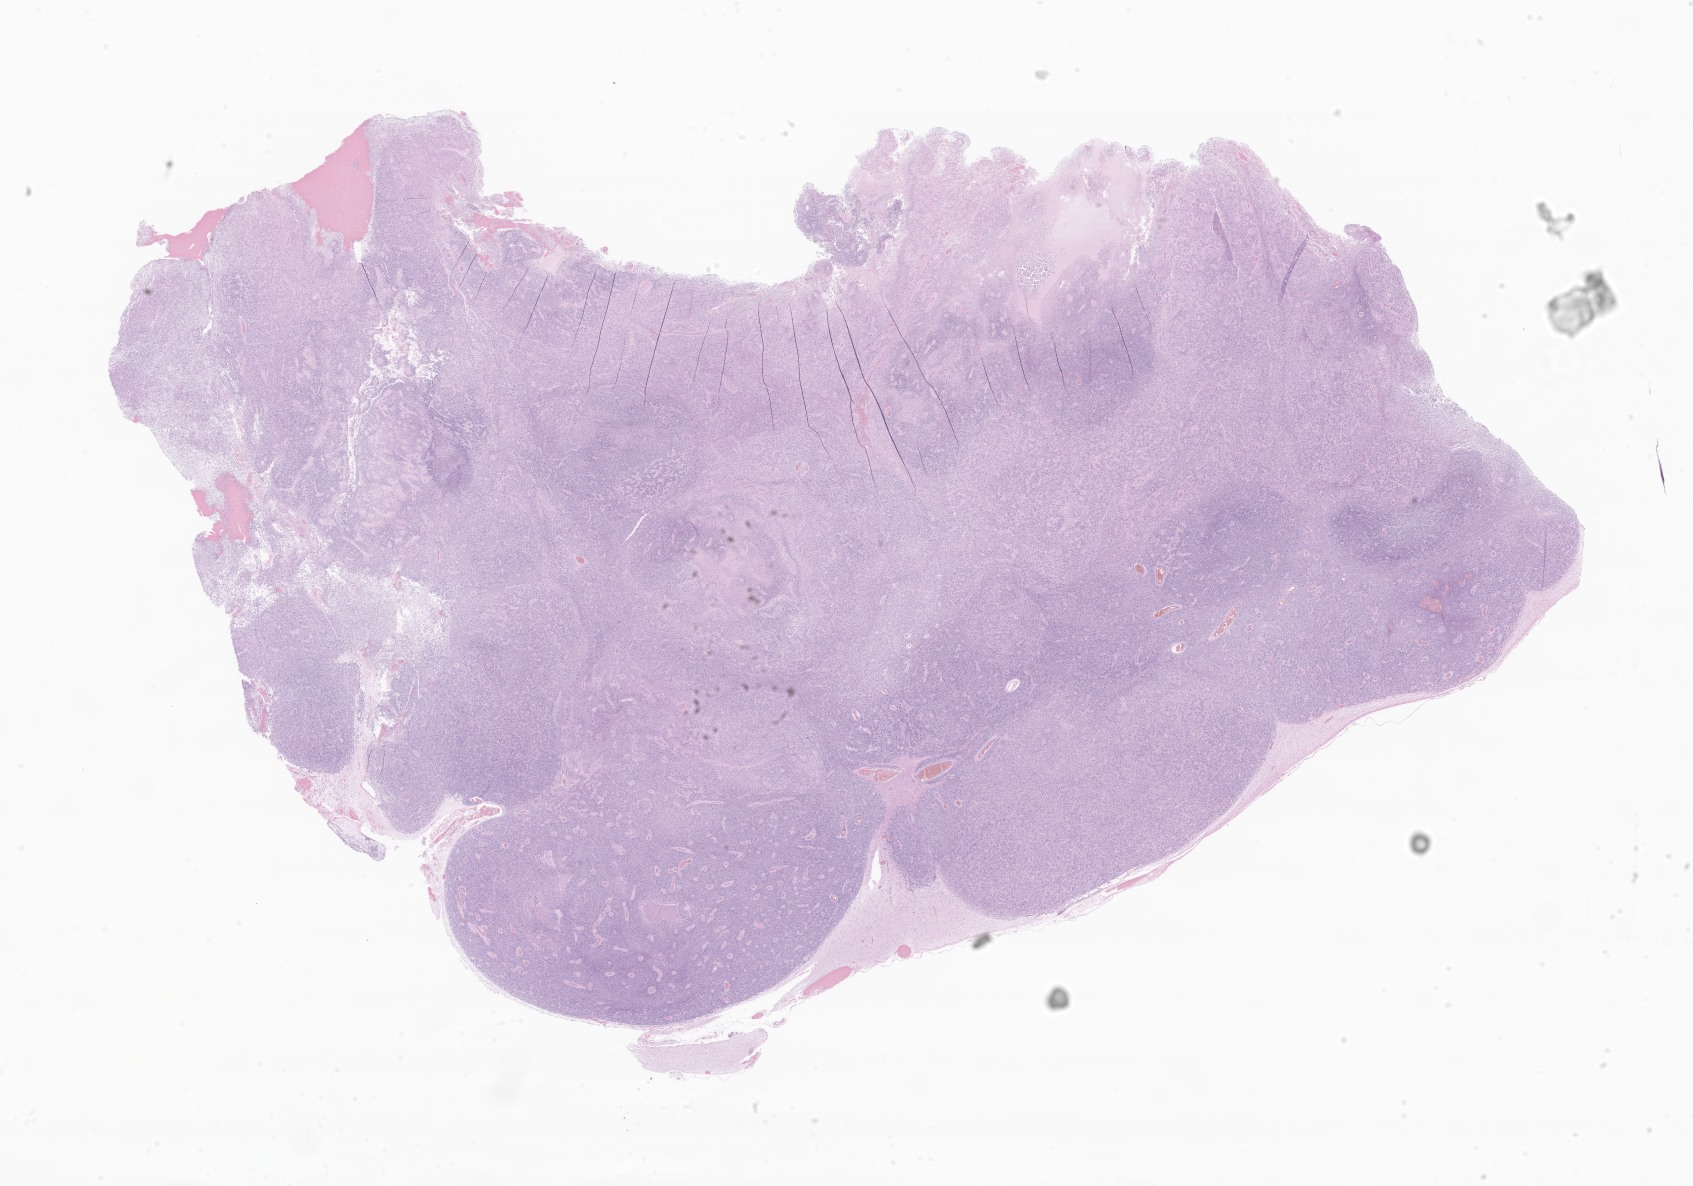
Whole-slide image, H&E stain of tumor tissue from the parietal lobe — shown as a low-resolution overview of the whole scanned area (about 28.6 x 20.0 mm). FFPE section. Patient: female, age 225 days.
Recorded diagnosis: Ependymoma, anaplastic.